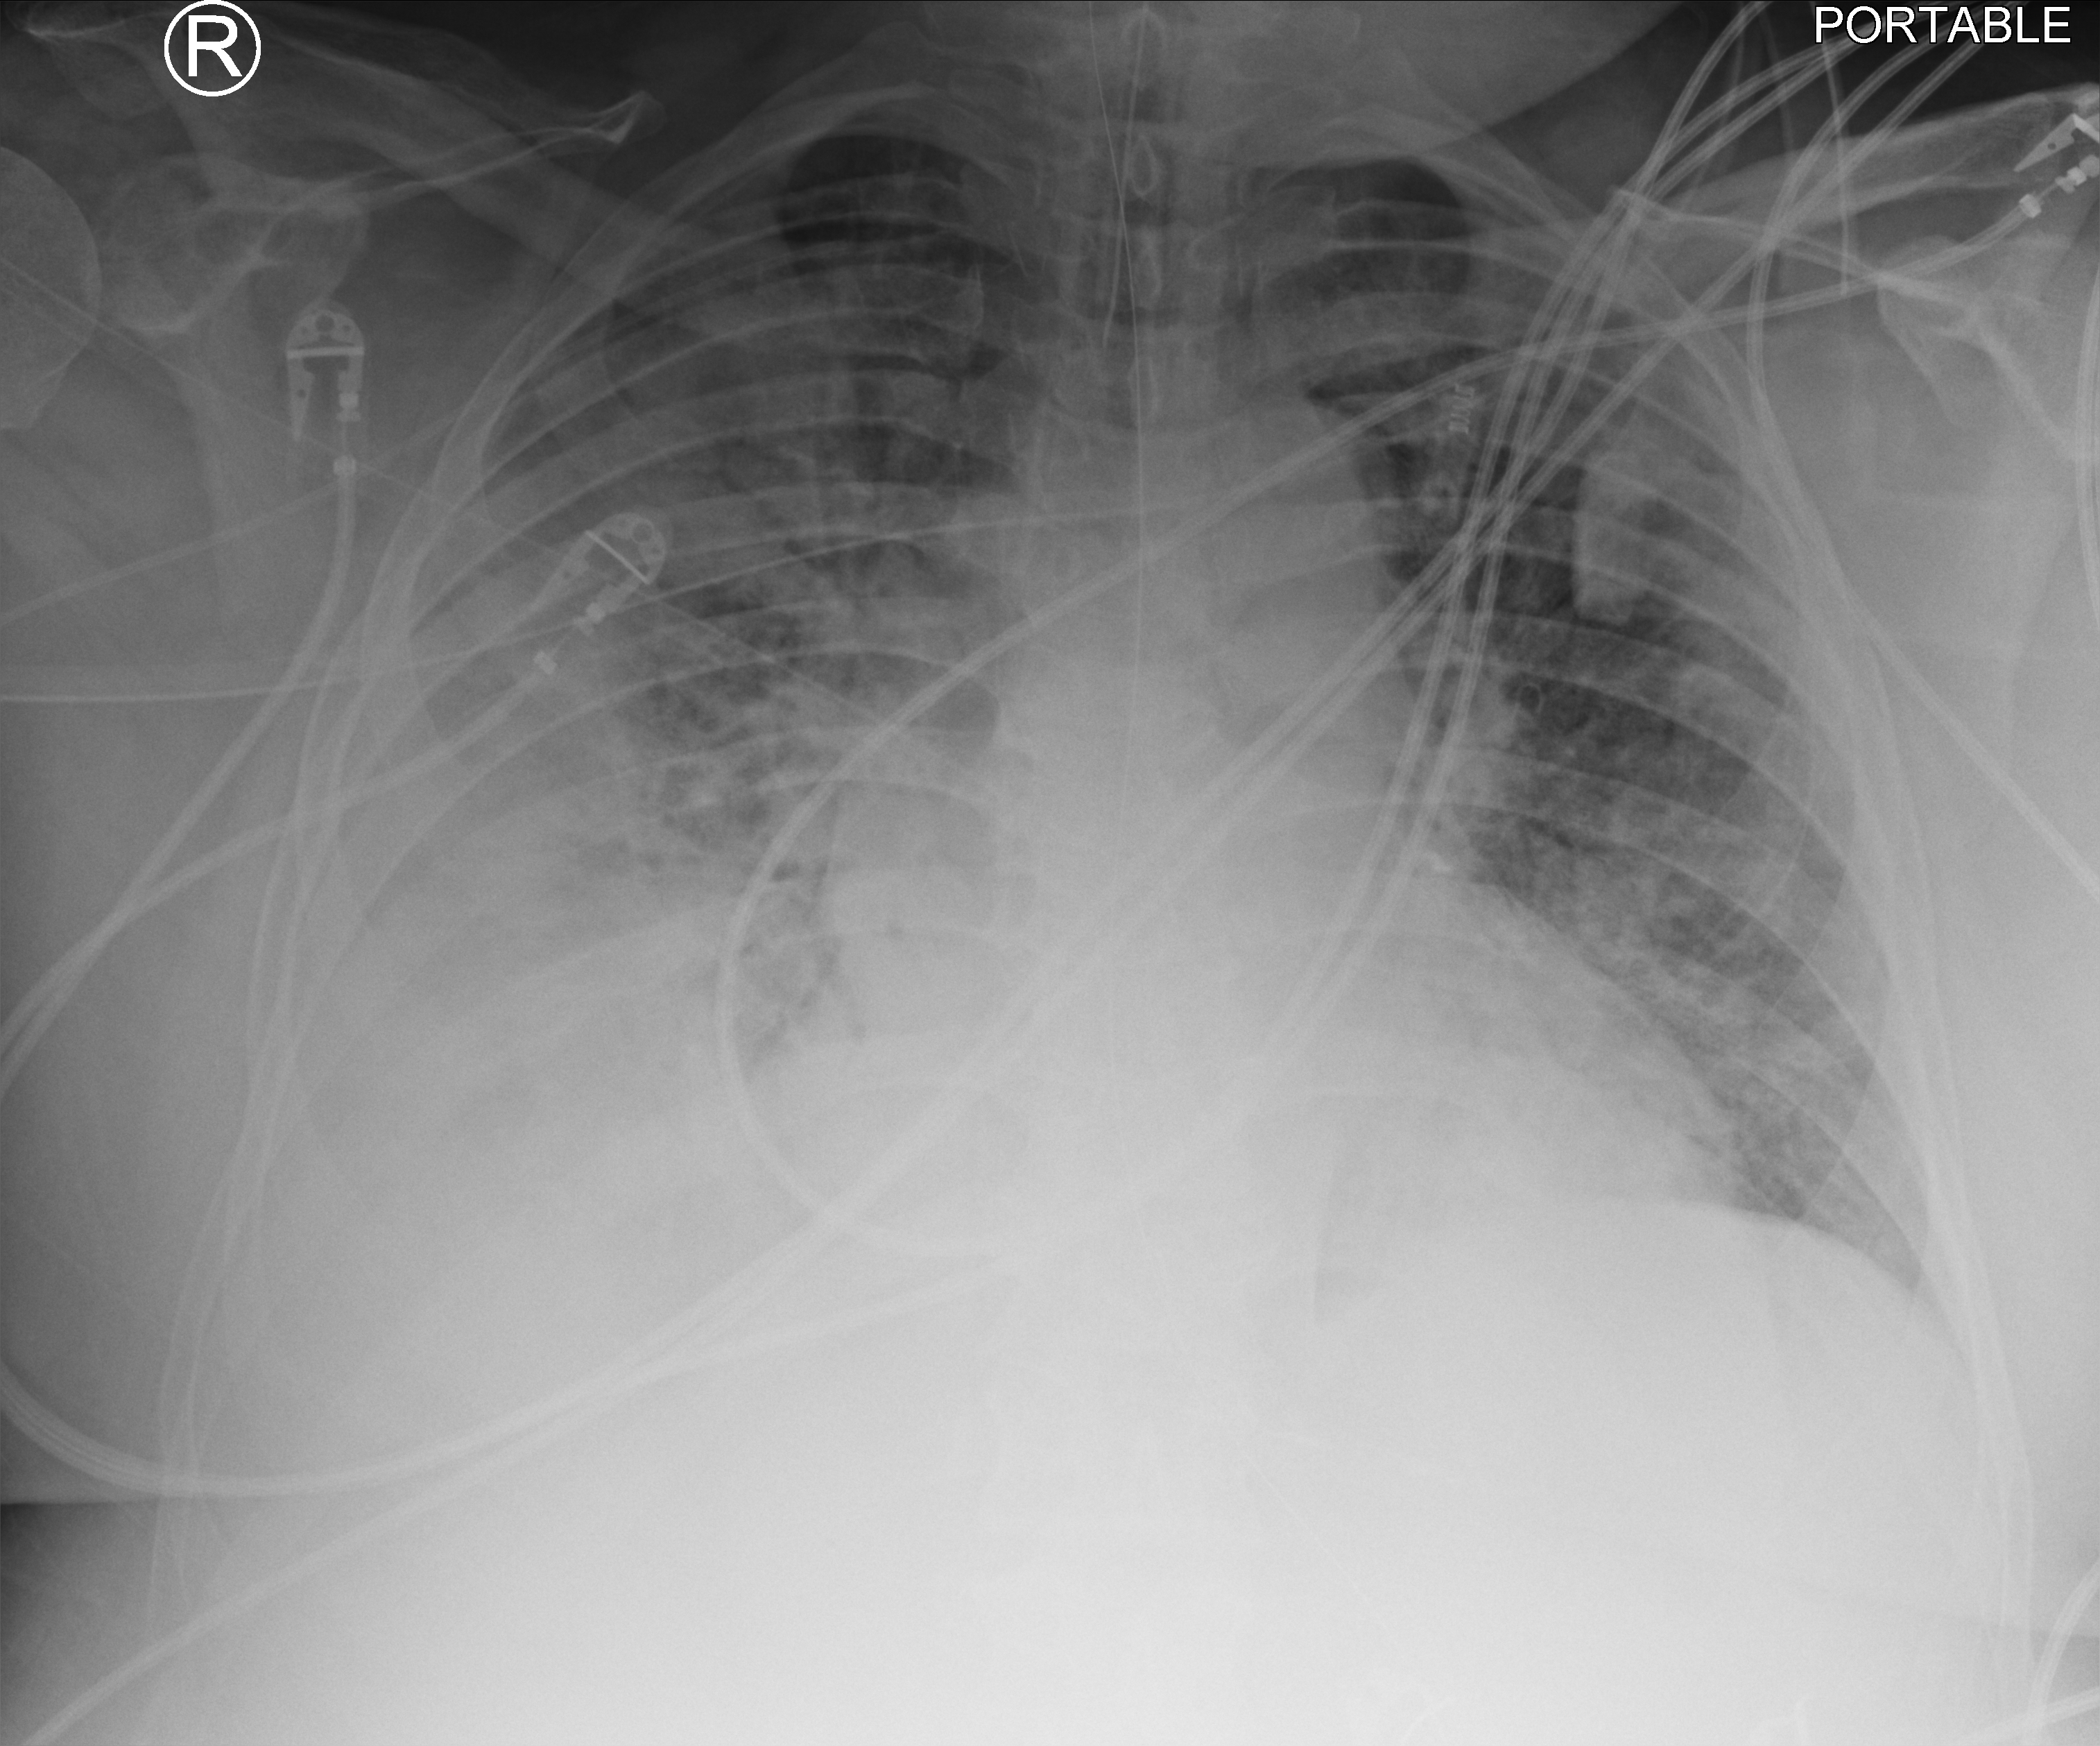
Chest X-ray (portable); anteroposterior (AP) projection. Patient hospitalised with COVID-19; male, aged 18–59 years.
Admission-level facts for this patient (not findings on this image; timing relative to this image not recorded): admitted to intensive care during this hospital stay: yes; mechanically ventilated during this hospital stay: yes.